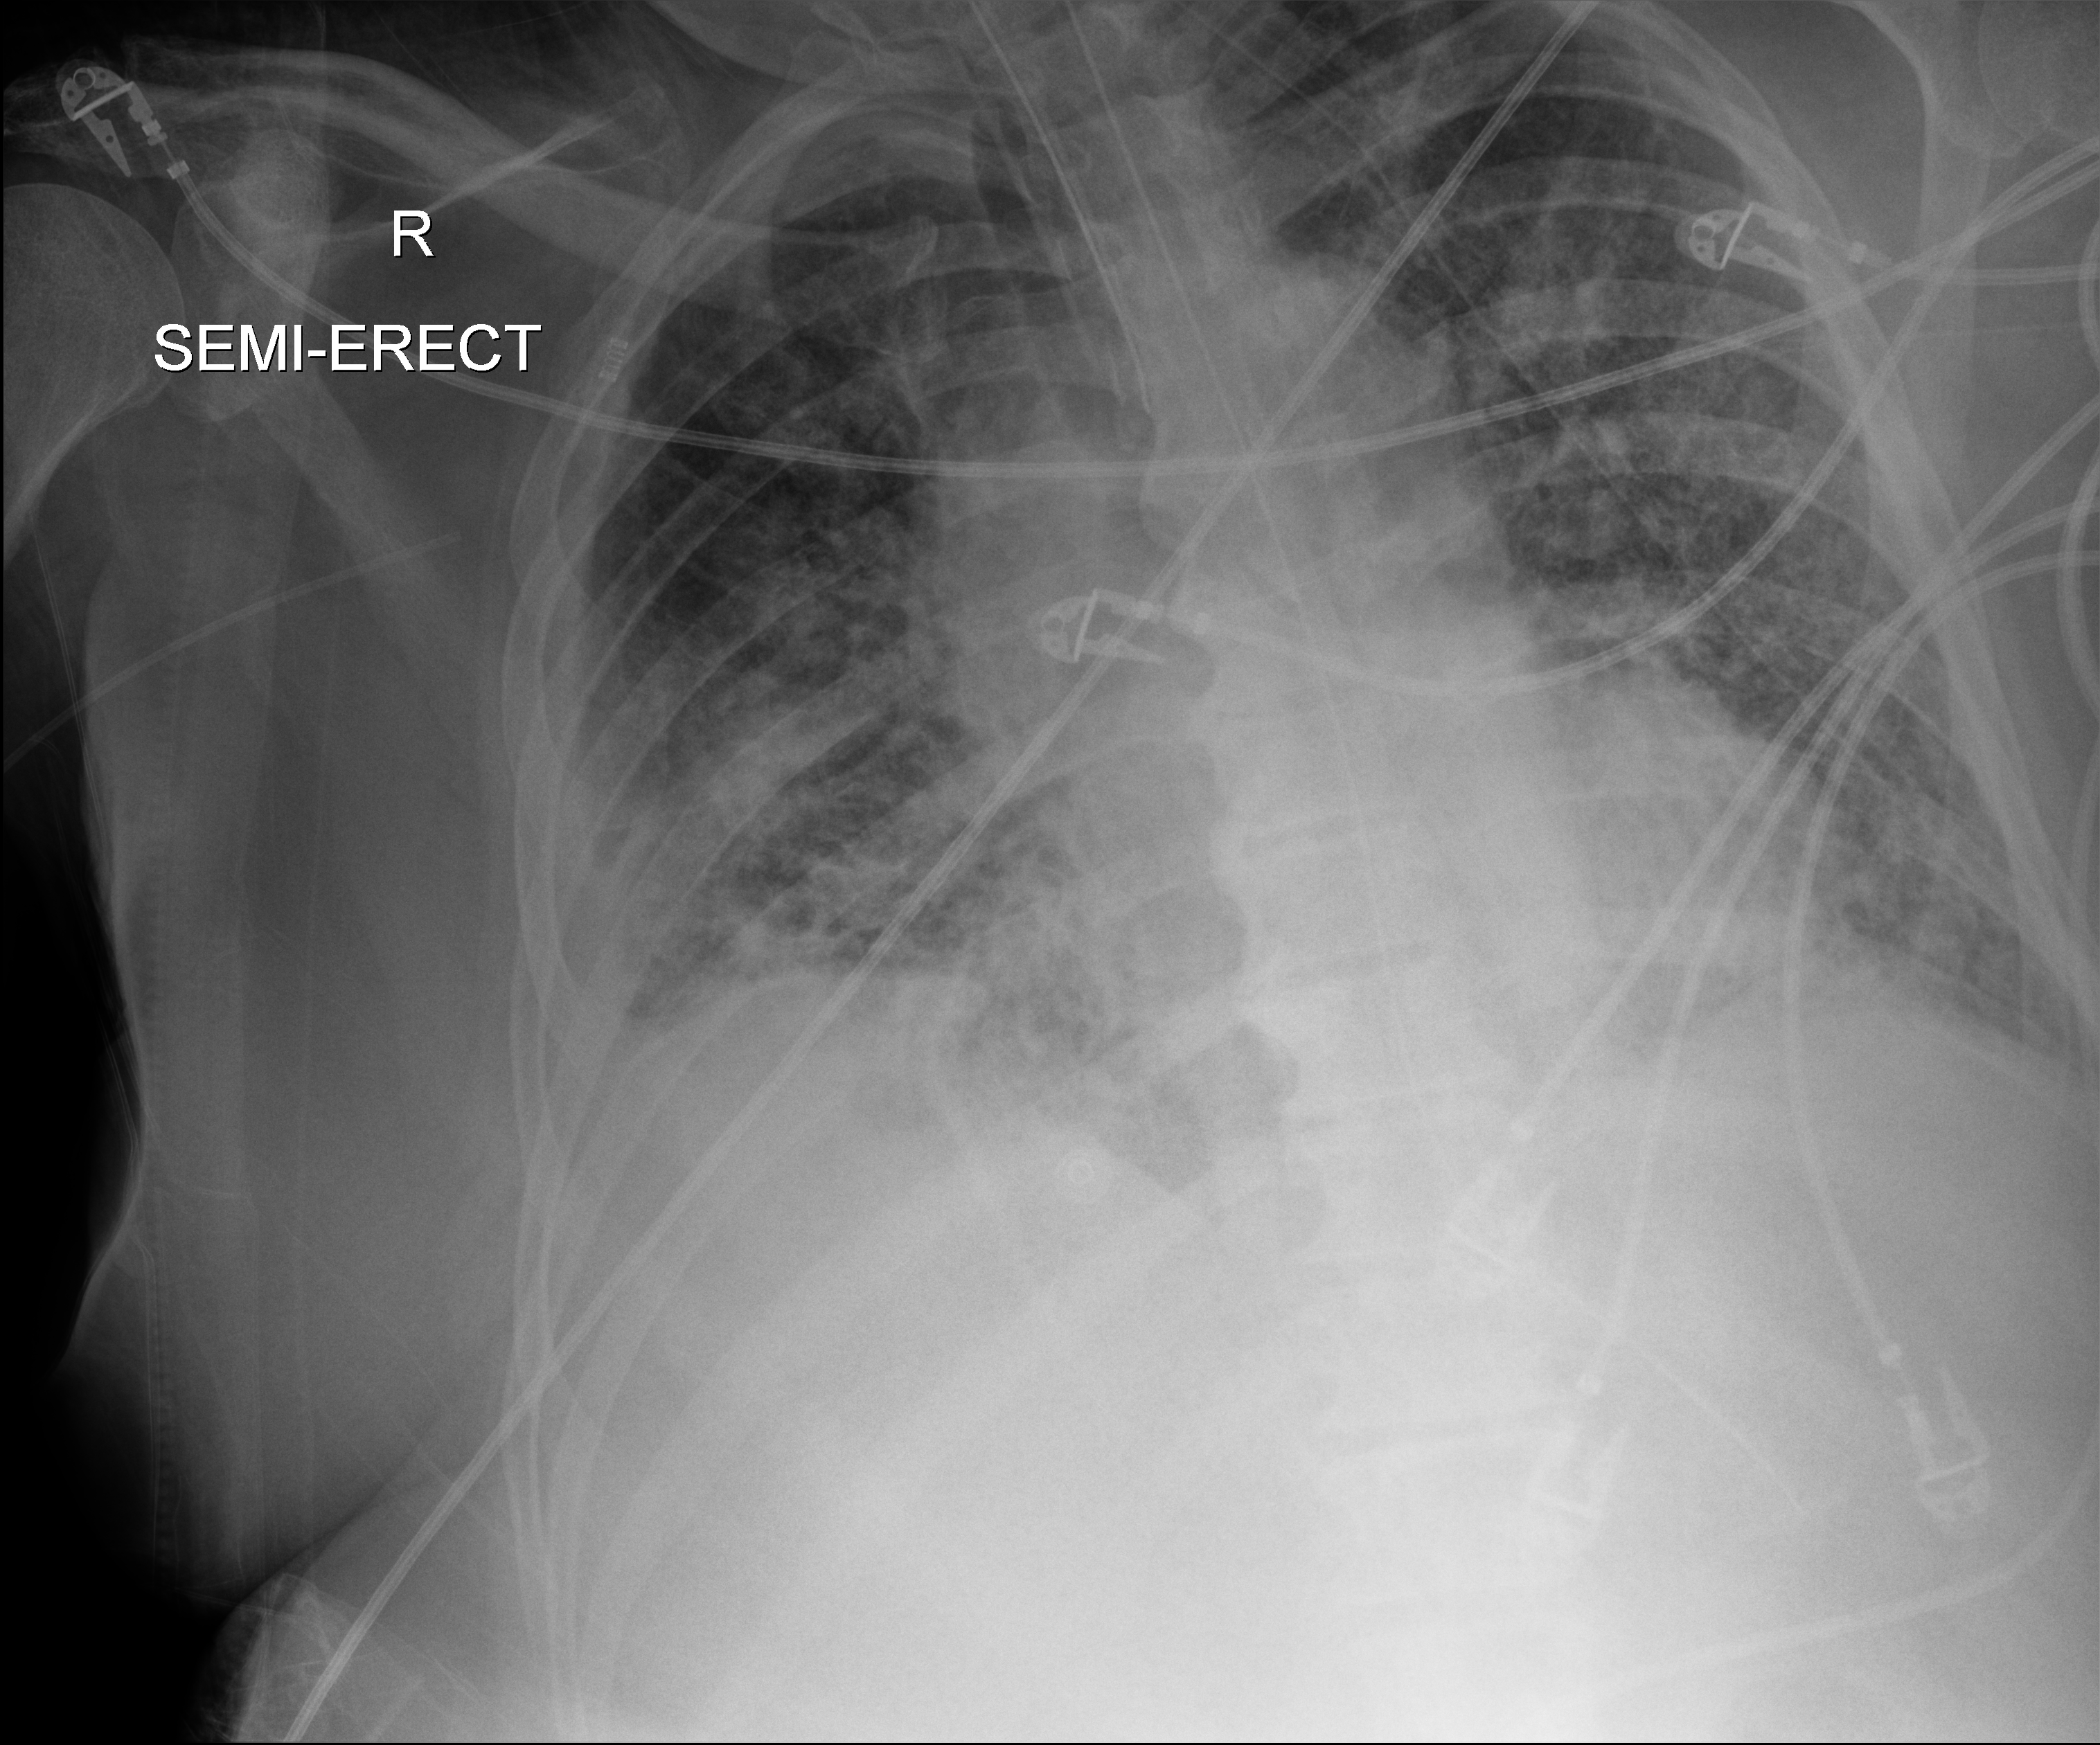
Portable chest radiograph. Male patient hospitalised with COVID-19, age 60–74 years.
Hospital-stay facts (about this admission, not read from this image; timing relative to this image not recorded):
- admitted to intensive care during this hospital stay: yes
- smoking status (admission record): former